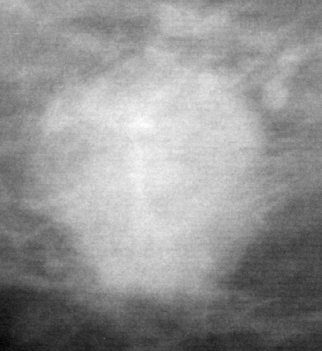
Cropped region of a digitized screen-film mammogram centred on a radiologist-marked abnormality, right breast, MLO view, BI-RADS breast density category 1 (scale 1–4).
- Finding: mass, shape oval, margins microlobulated; BI-RADS assessment category 4; subtlety rating 5 on a 1 (subtle) to 5 (obvious) scale; pathology (as recorded): malignant.